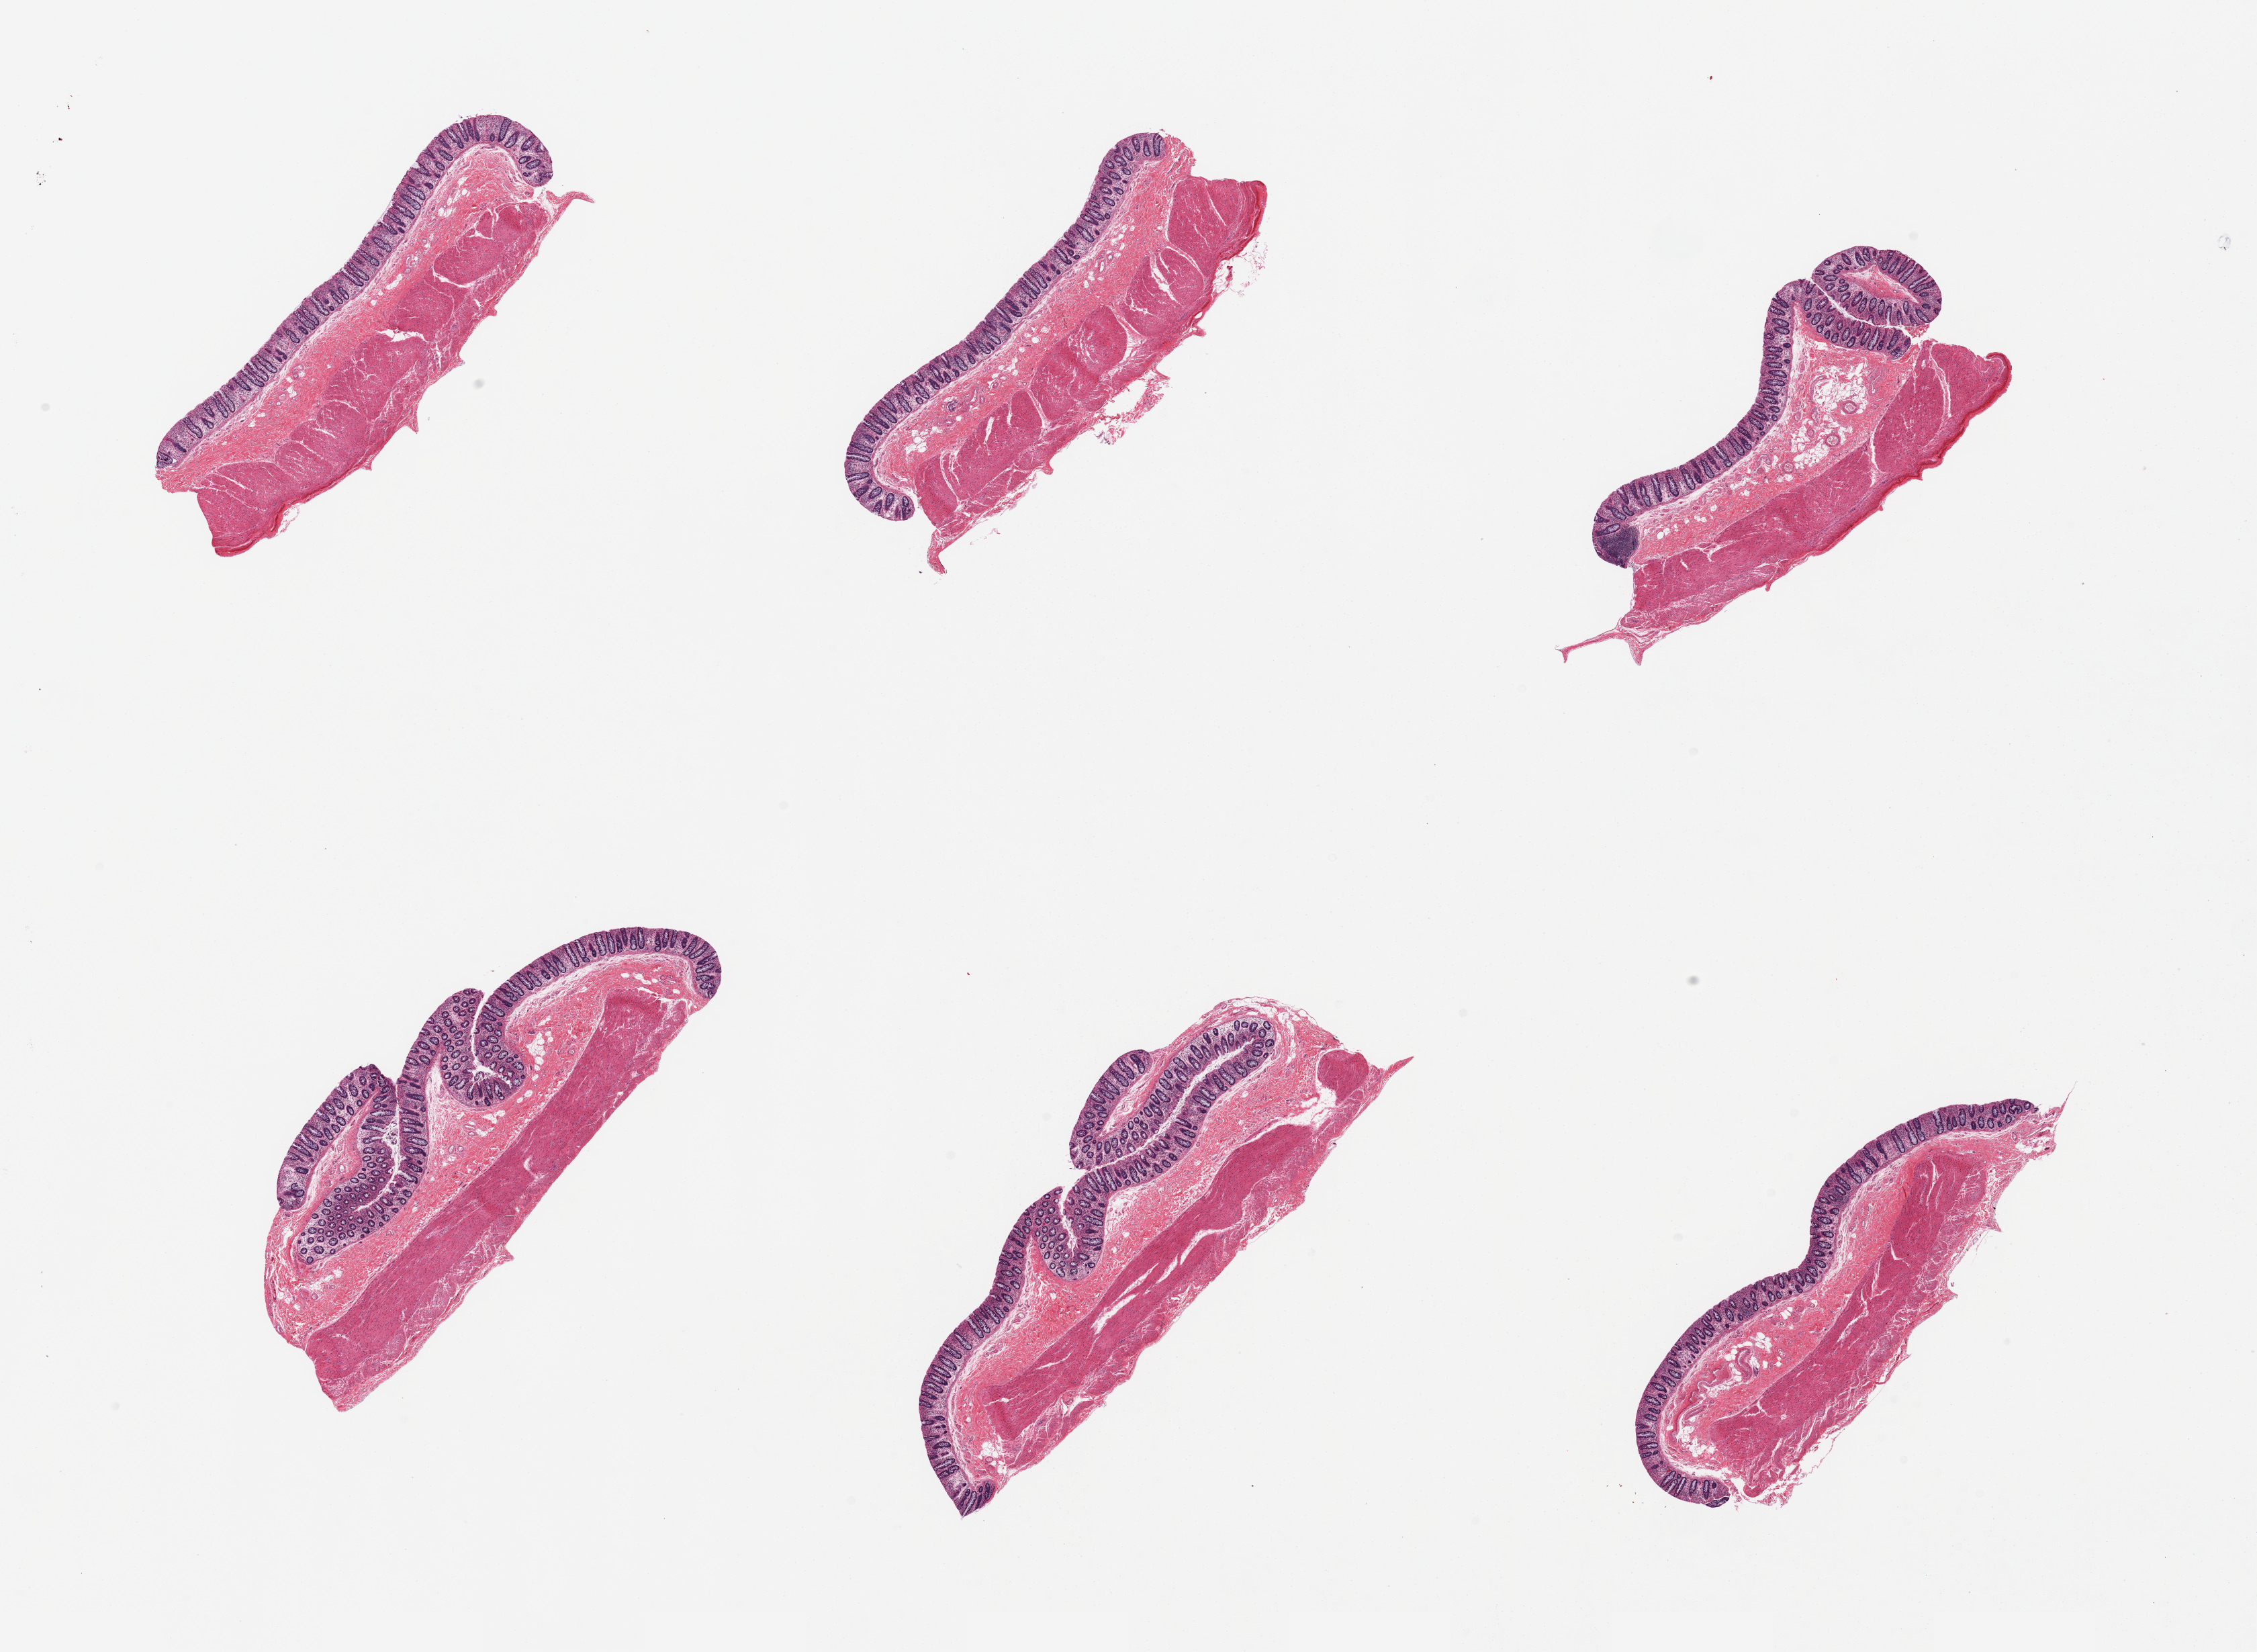
Hematoxylin and eosin (H&E) whole-slide image, low-resolution overview of the scanned area, about 26.6 x 19.5 mm, PAXgene-fixed, paraffin-embedded tissue, target tissue: transverse colon, donor tissue sample. Donor: male.
Review note (as recorded): 6 pieces, mucosa (autolysis 1-2) and muscularis.